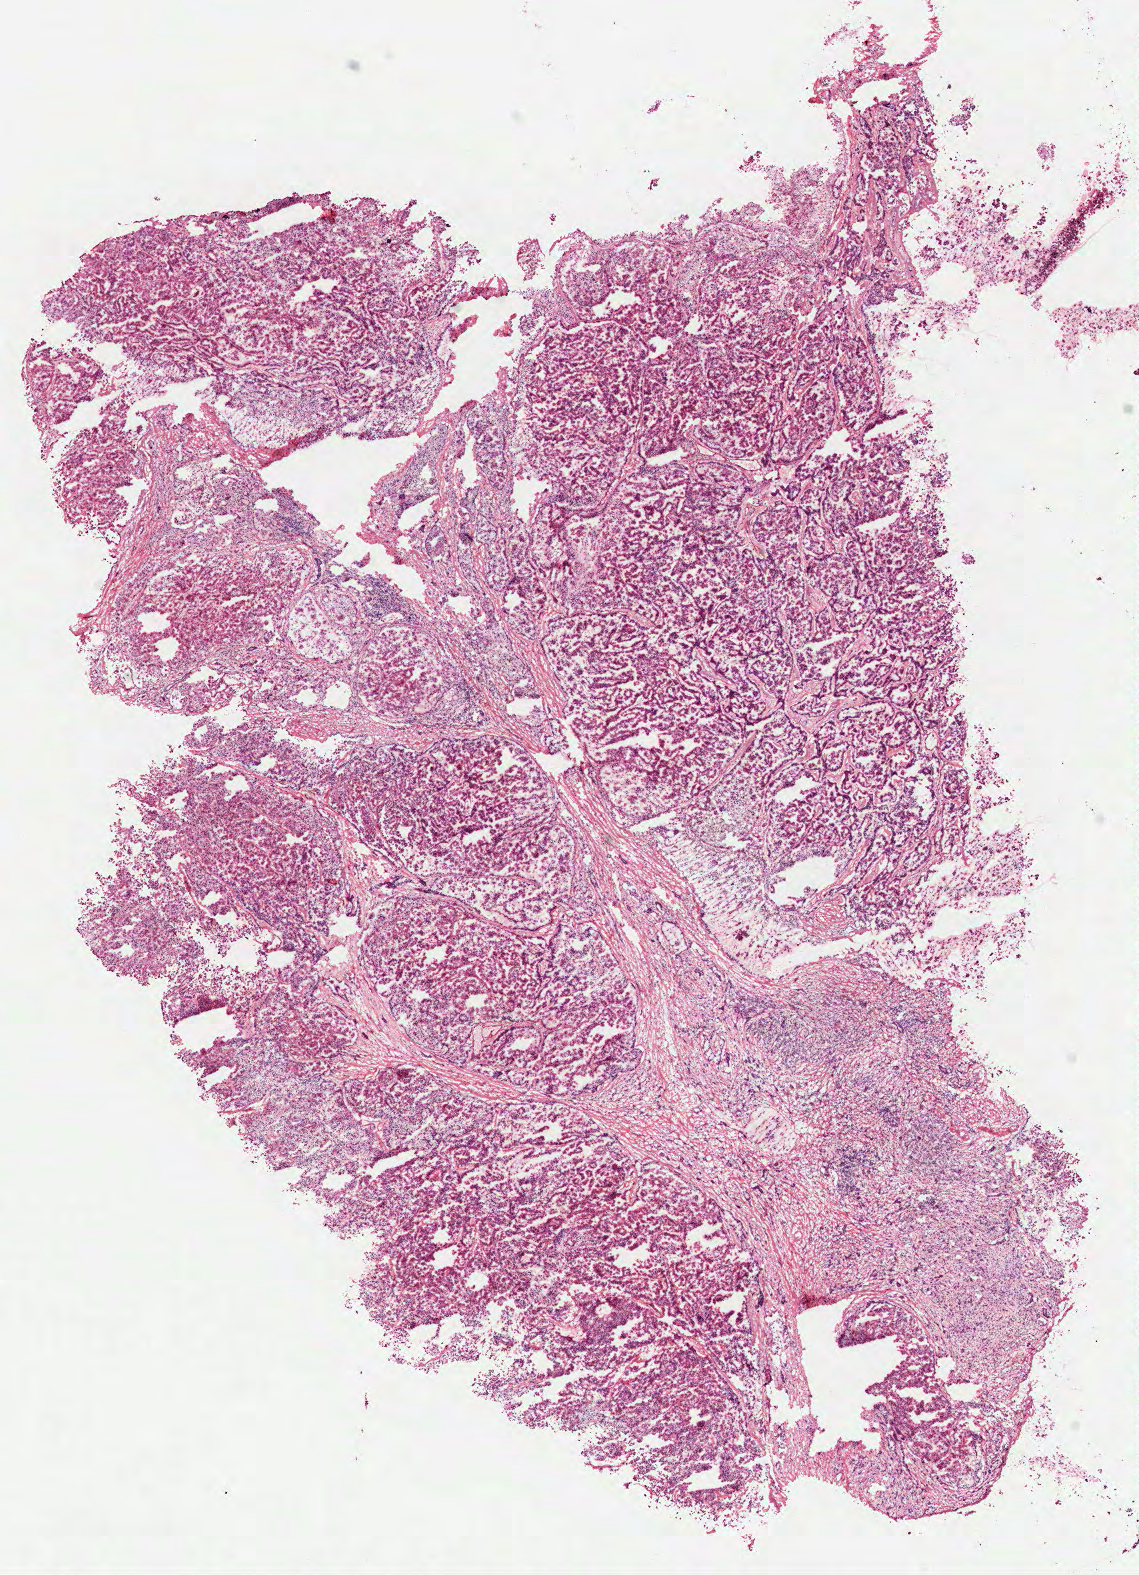
Whole-slide histology image, H&E — whole scanned area (about 9.2 x 12.7 mm) shown as a low-resolution overview, frozen section from the top of the tissue portion, kidney, primary tumour sample. Female, age 83 years at initial diagnosis. Slide review estimates, as recorded: tumour cells 100%, tumour nuclei 65%, normal cells 0%, stromal cells 0%, necrosis 0%. Inflammatory infiltration, as recorded: lymphocyte infiltration 0%, monocyte infiltration 20%, neutrophil infiltration 0%.
Histologic diagnosis: Papillary adenocarcinoma, NOS. Laterality: left. AJCC pathologic stage: I.